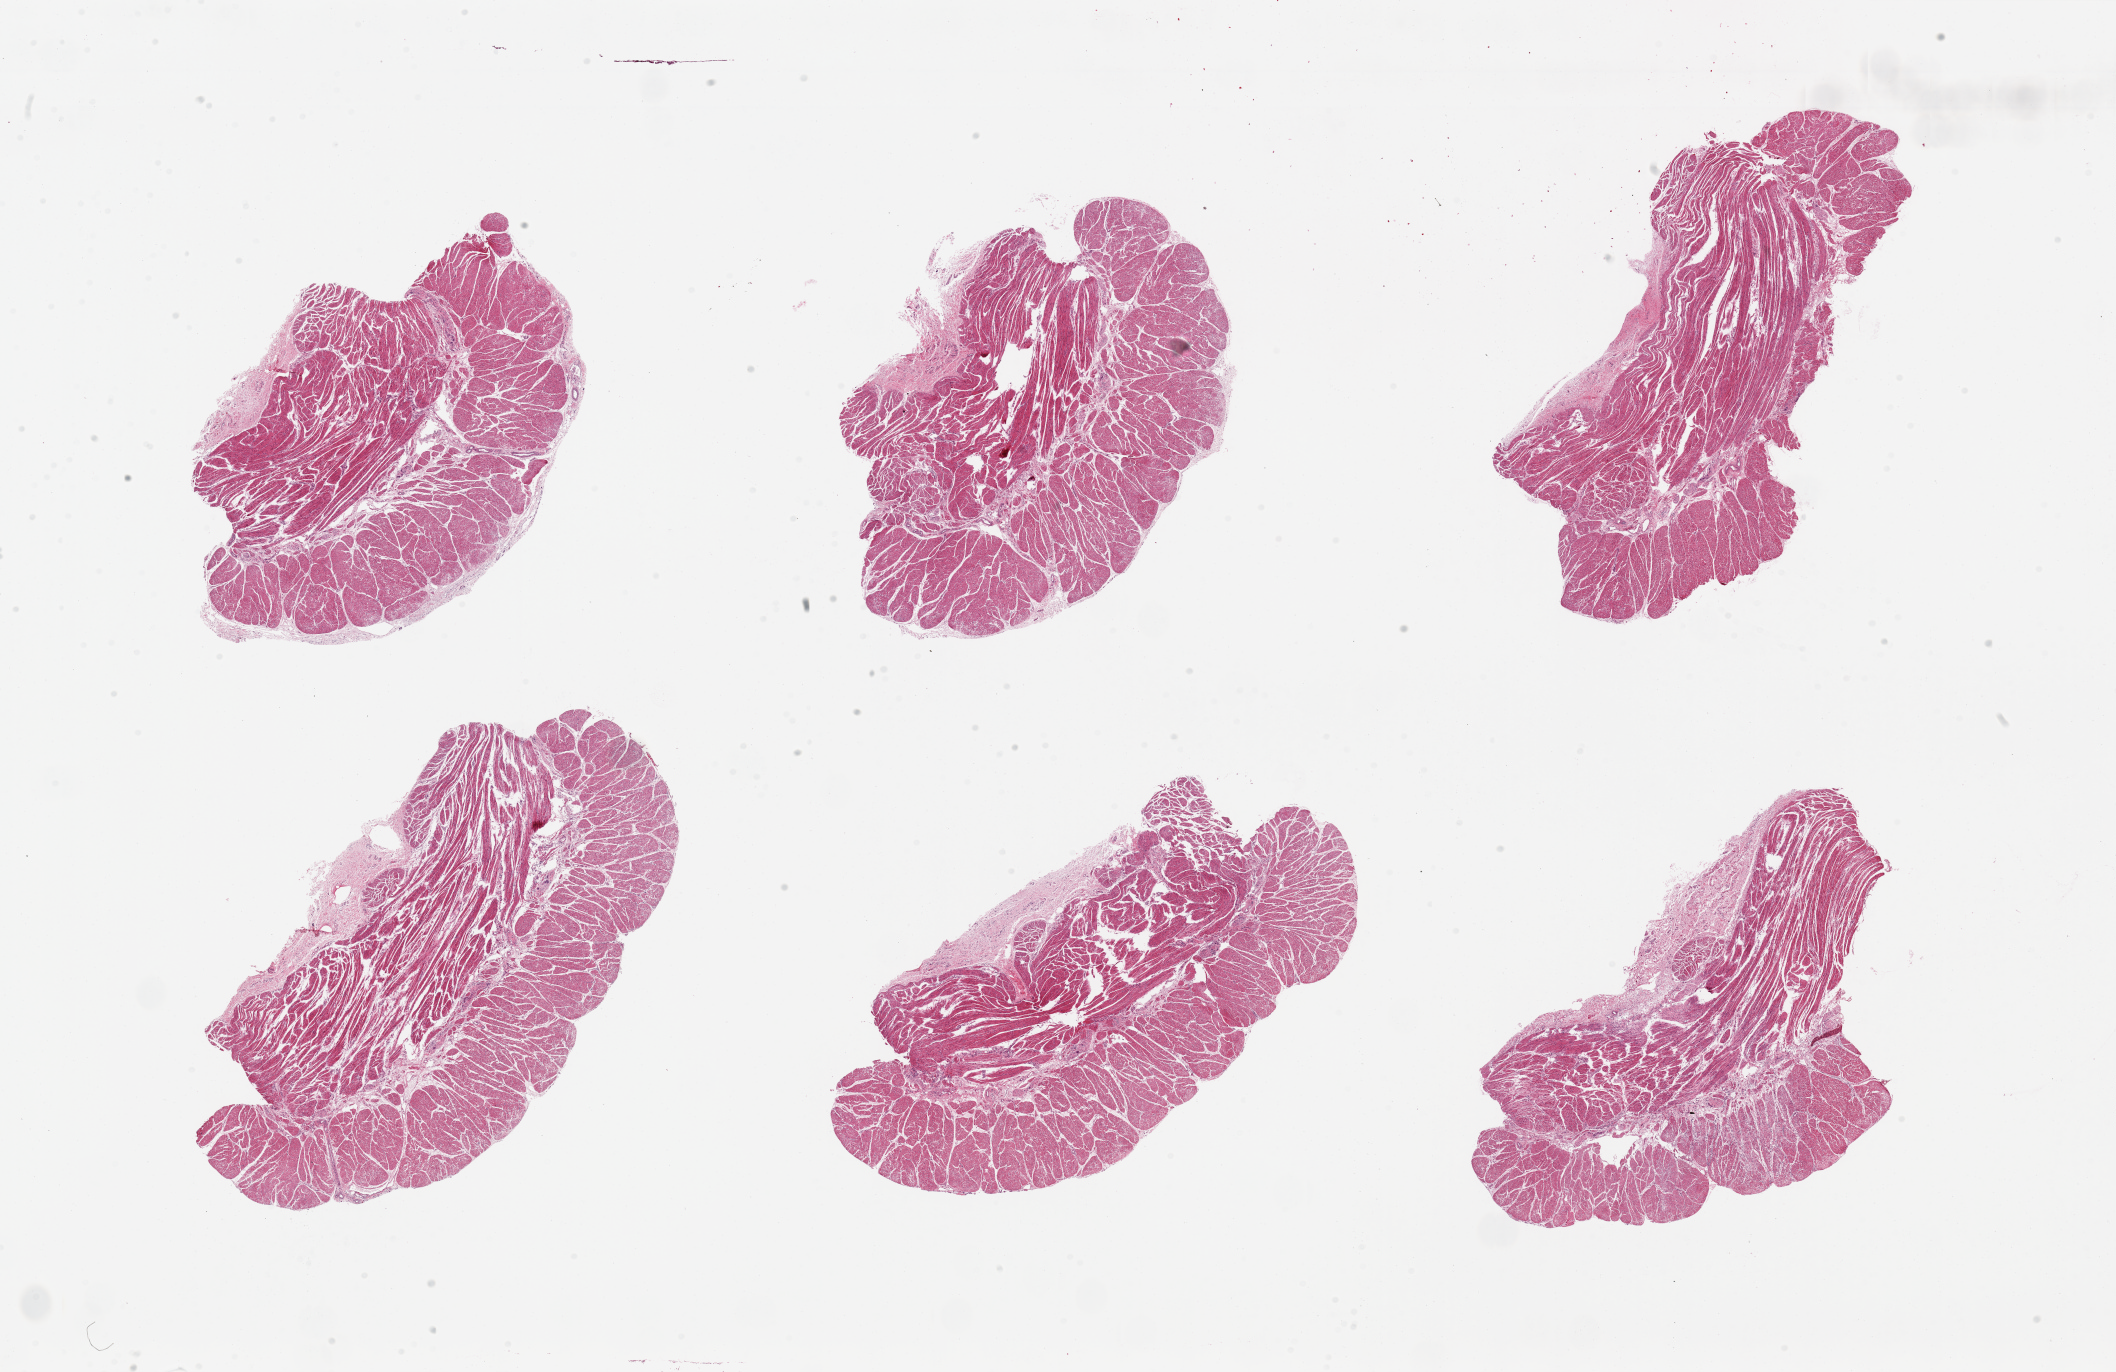
Whole-slide image, hematoxylin and eosin (H&E) stain, brightfield — whole scanned area (about 33.5 x 21.7 mm) shown as a low-resolution overview. PAXgene-fixed, paraffin-embedded tissue. Target tissue: esophageal muscle. Donor tissue sample. Donor: male.
- pathologist's review note for this sample: 6 pieces, up to 10x5mm; all muscularis, good specimens